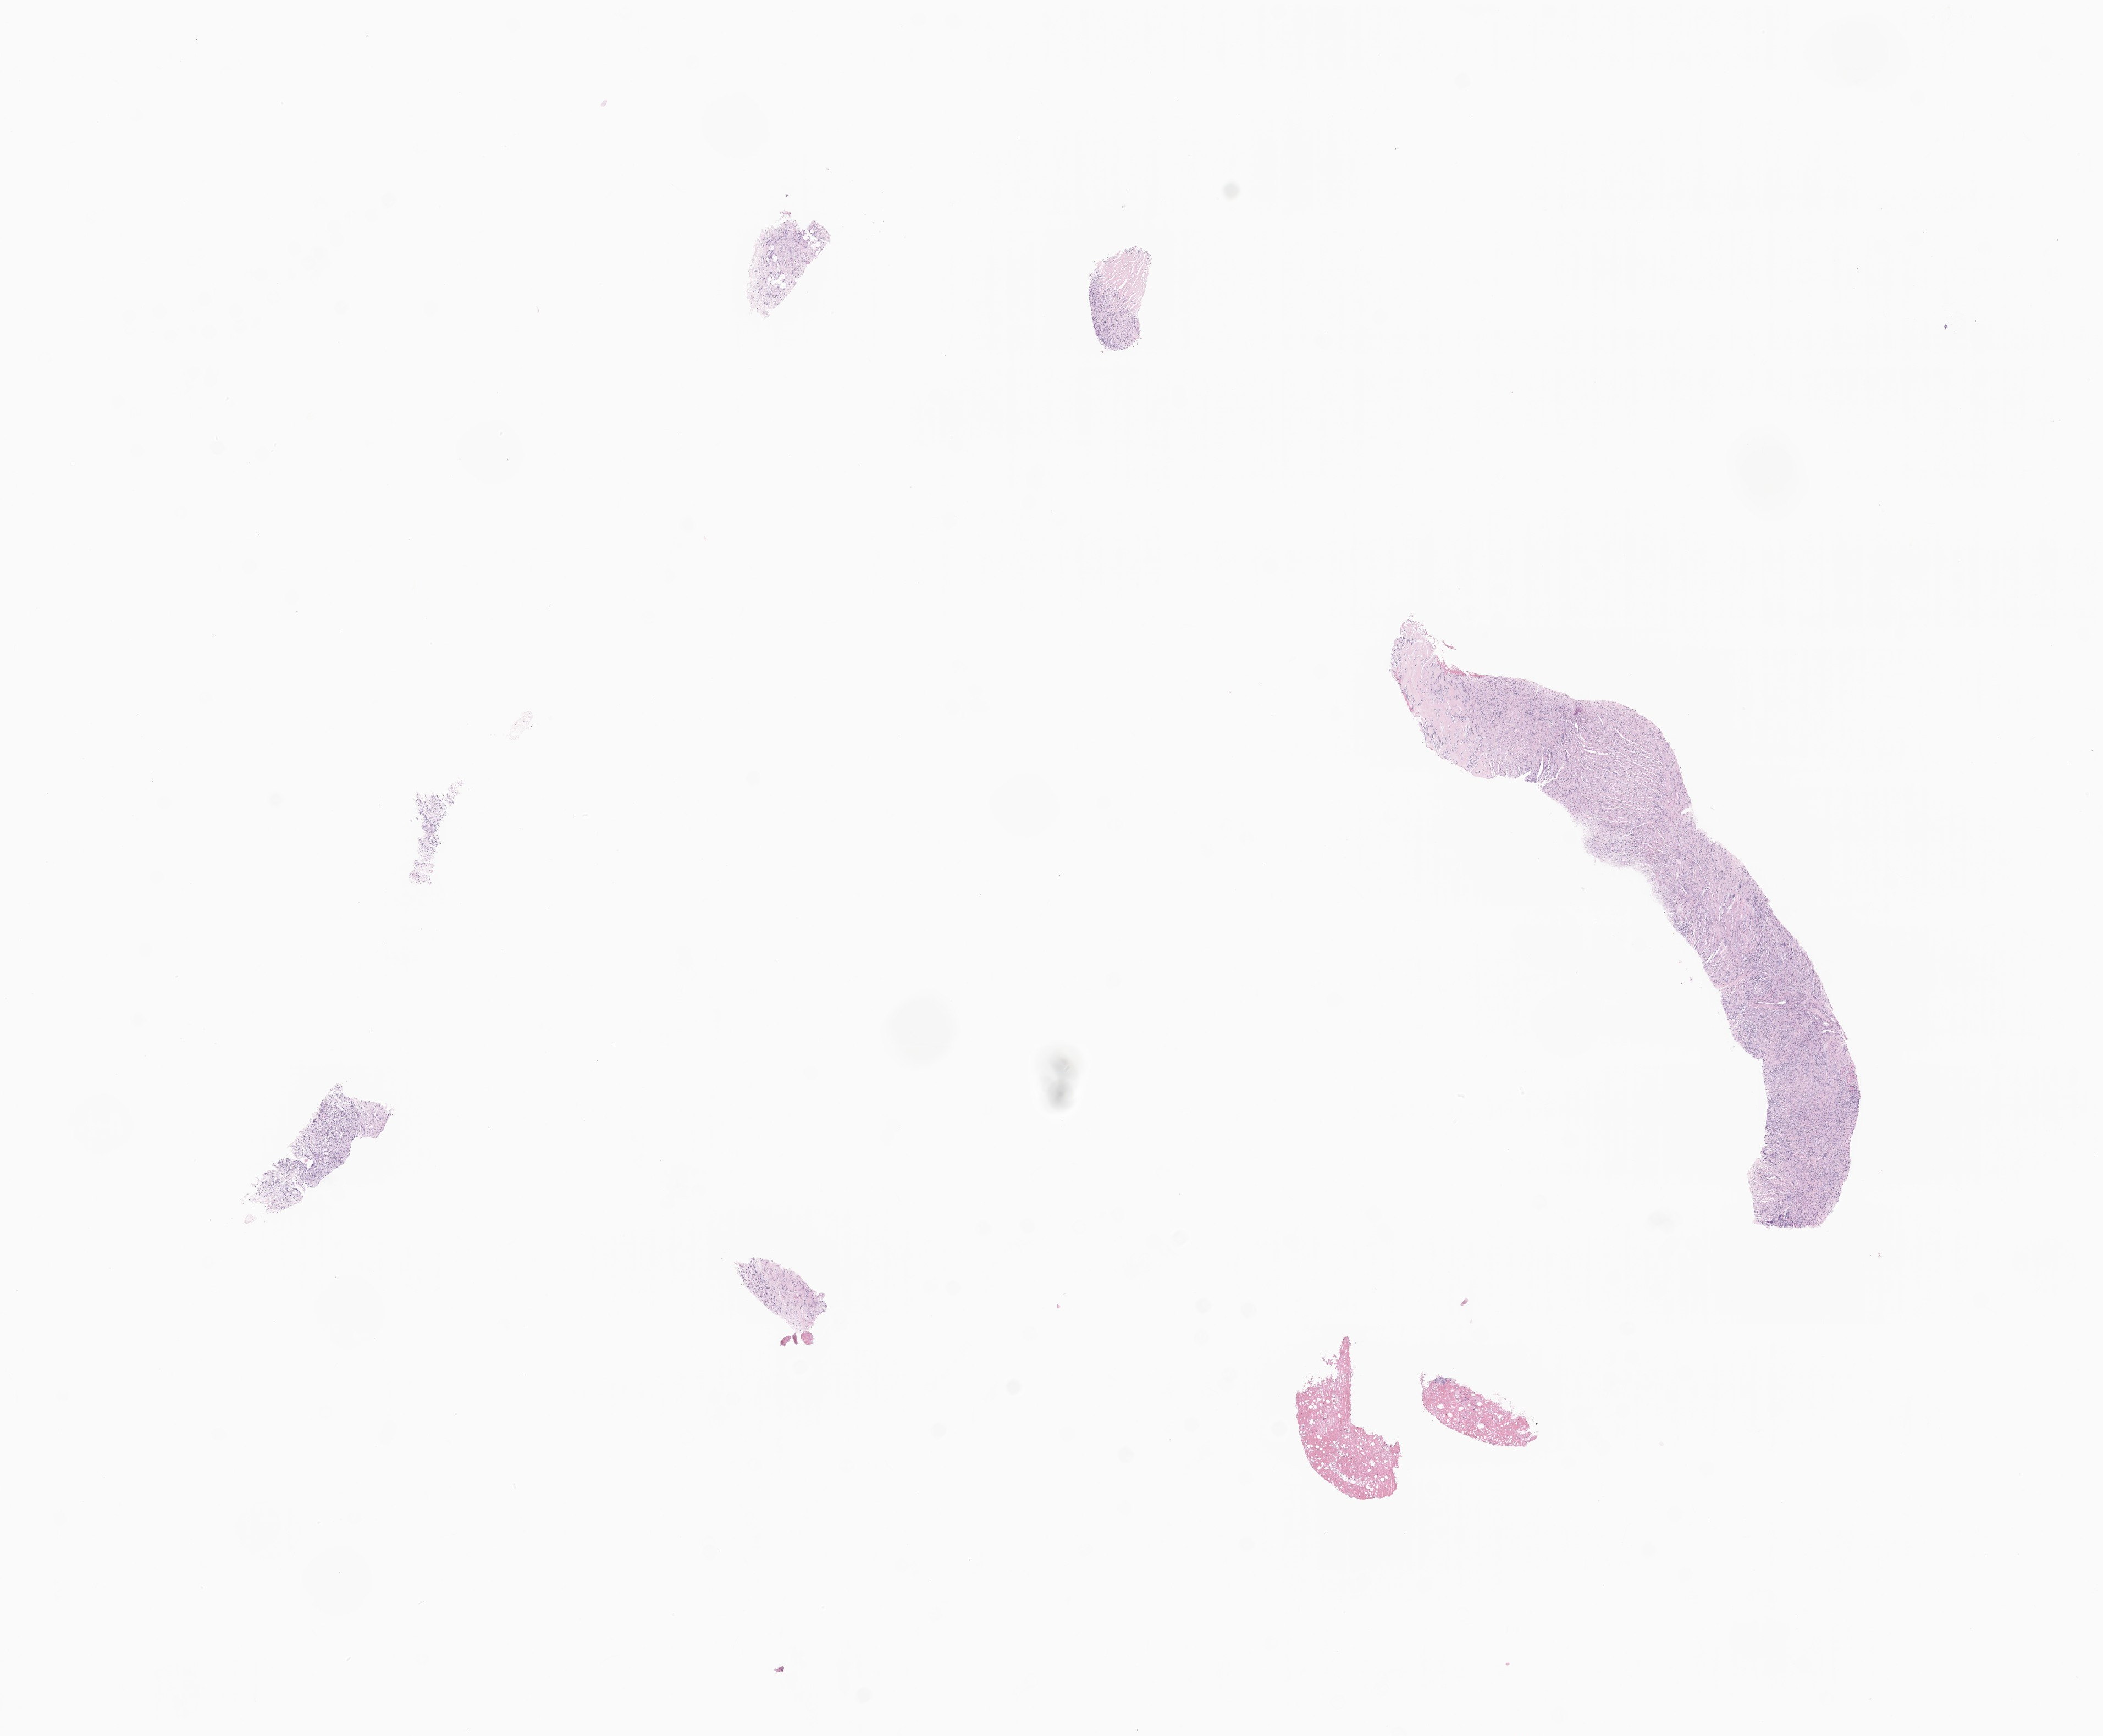
Whole-slide image, haematoxylin and eosin stain of tumor tissue from the soft tissue of upper extremity, low-resolution overview of the scanned area, about 16.1 x 13.3 mm; FFPE section. Patient female; age 192 months (16 years).
Diagnosis: Myofibroblastic tumor, NOS.